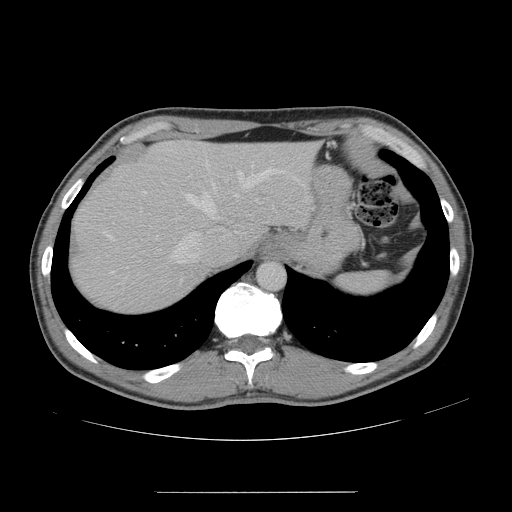
Contrast-enhanced abdominal CT, one axial slice; position 123 of 178 along the scan axis; soft-tissue window (W 400 / L 40 HU); 2.5 mm slice thickness; 512 × 512 image matrix, field of view 401 × 401 mm. Male patient, age 53 years. From the clinical record (not read from this slice): diagnosis: colorectal cancer liver metastases, imaged before liver resection; multiple liver metastases: yes; largest metastasis: 2.4 cm.
Structures marked on this image (manually delineated by an expert):
- hepatic veins: box from (x=104, y=168) to (x=276, y=264) px
- liver: (x=71, y=141)–(x=319, y=312)
- planned liver remnant (the part of the liver to remain after resection): (x=153, y=141)–(x=317, y=245)